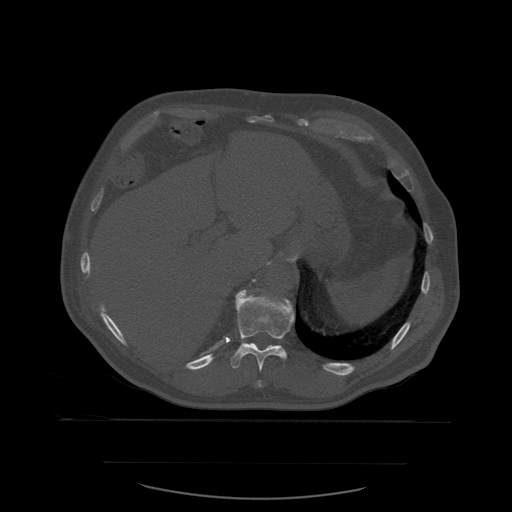
CT including the spine, one axial slice. Position 294 of 590 along the scan axis. Bone window (W 1800 / L 400 HU). 1.25 mm slice thickness. 512 × 512 image matrix, field of view 479 × 479 mm. Patient age 71 years. From the clinical record (not read from this slice): primary cancer: lung; vertebrae with lytic lesions (as recorded): T1, T2, L5, S1.
Outlined on this slice (semi-automatically segmented with operator editing):
- T10 vertebra: bounding box (x1, y1, x2, y2) in pixels: (258, 381, 263, 388)
- T11 vertebra: (230, 289, 295, 388)
- T12 vertebra: (252, 294, 278, 344)